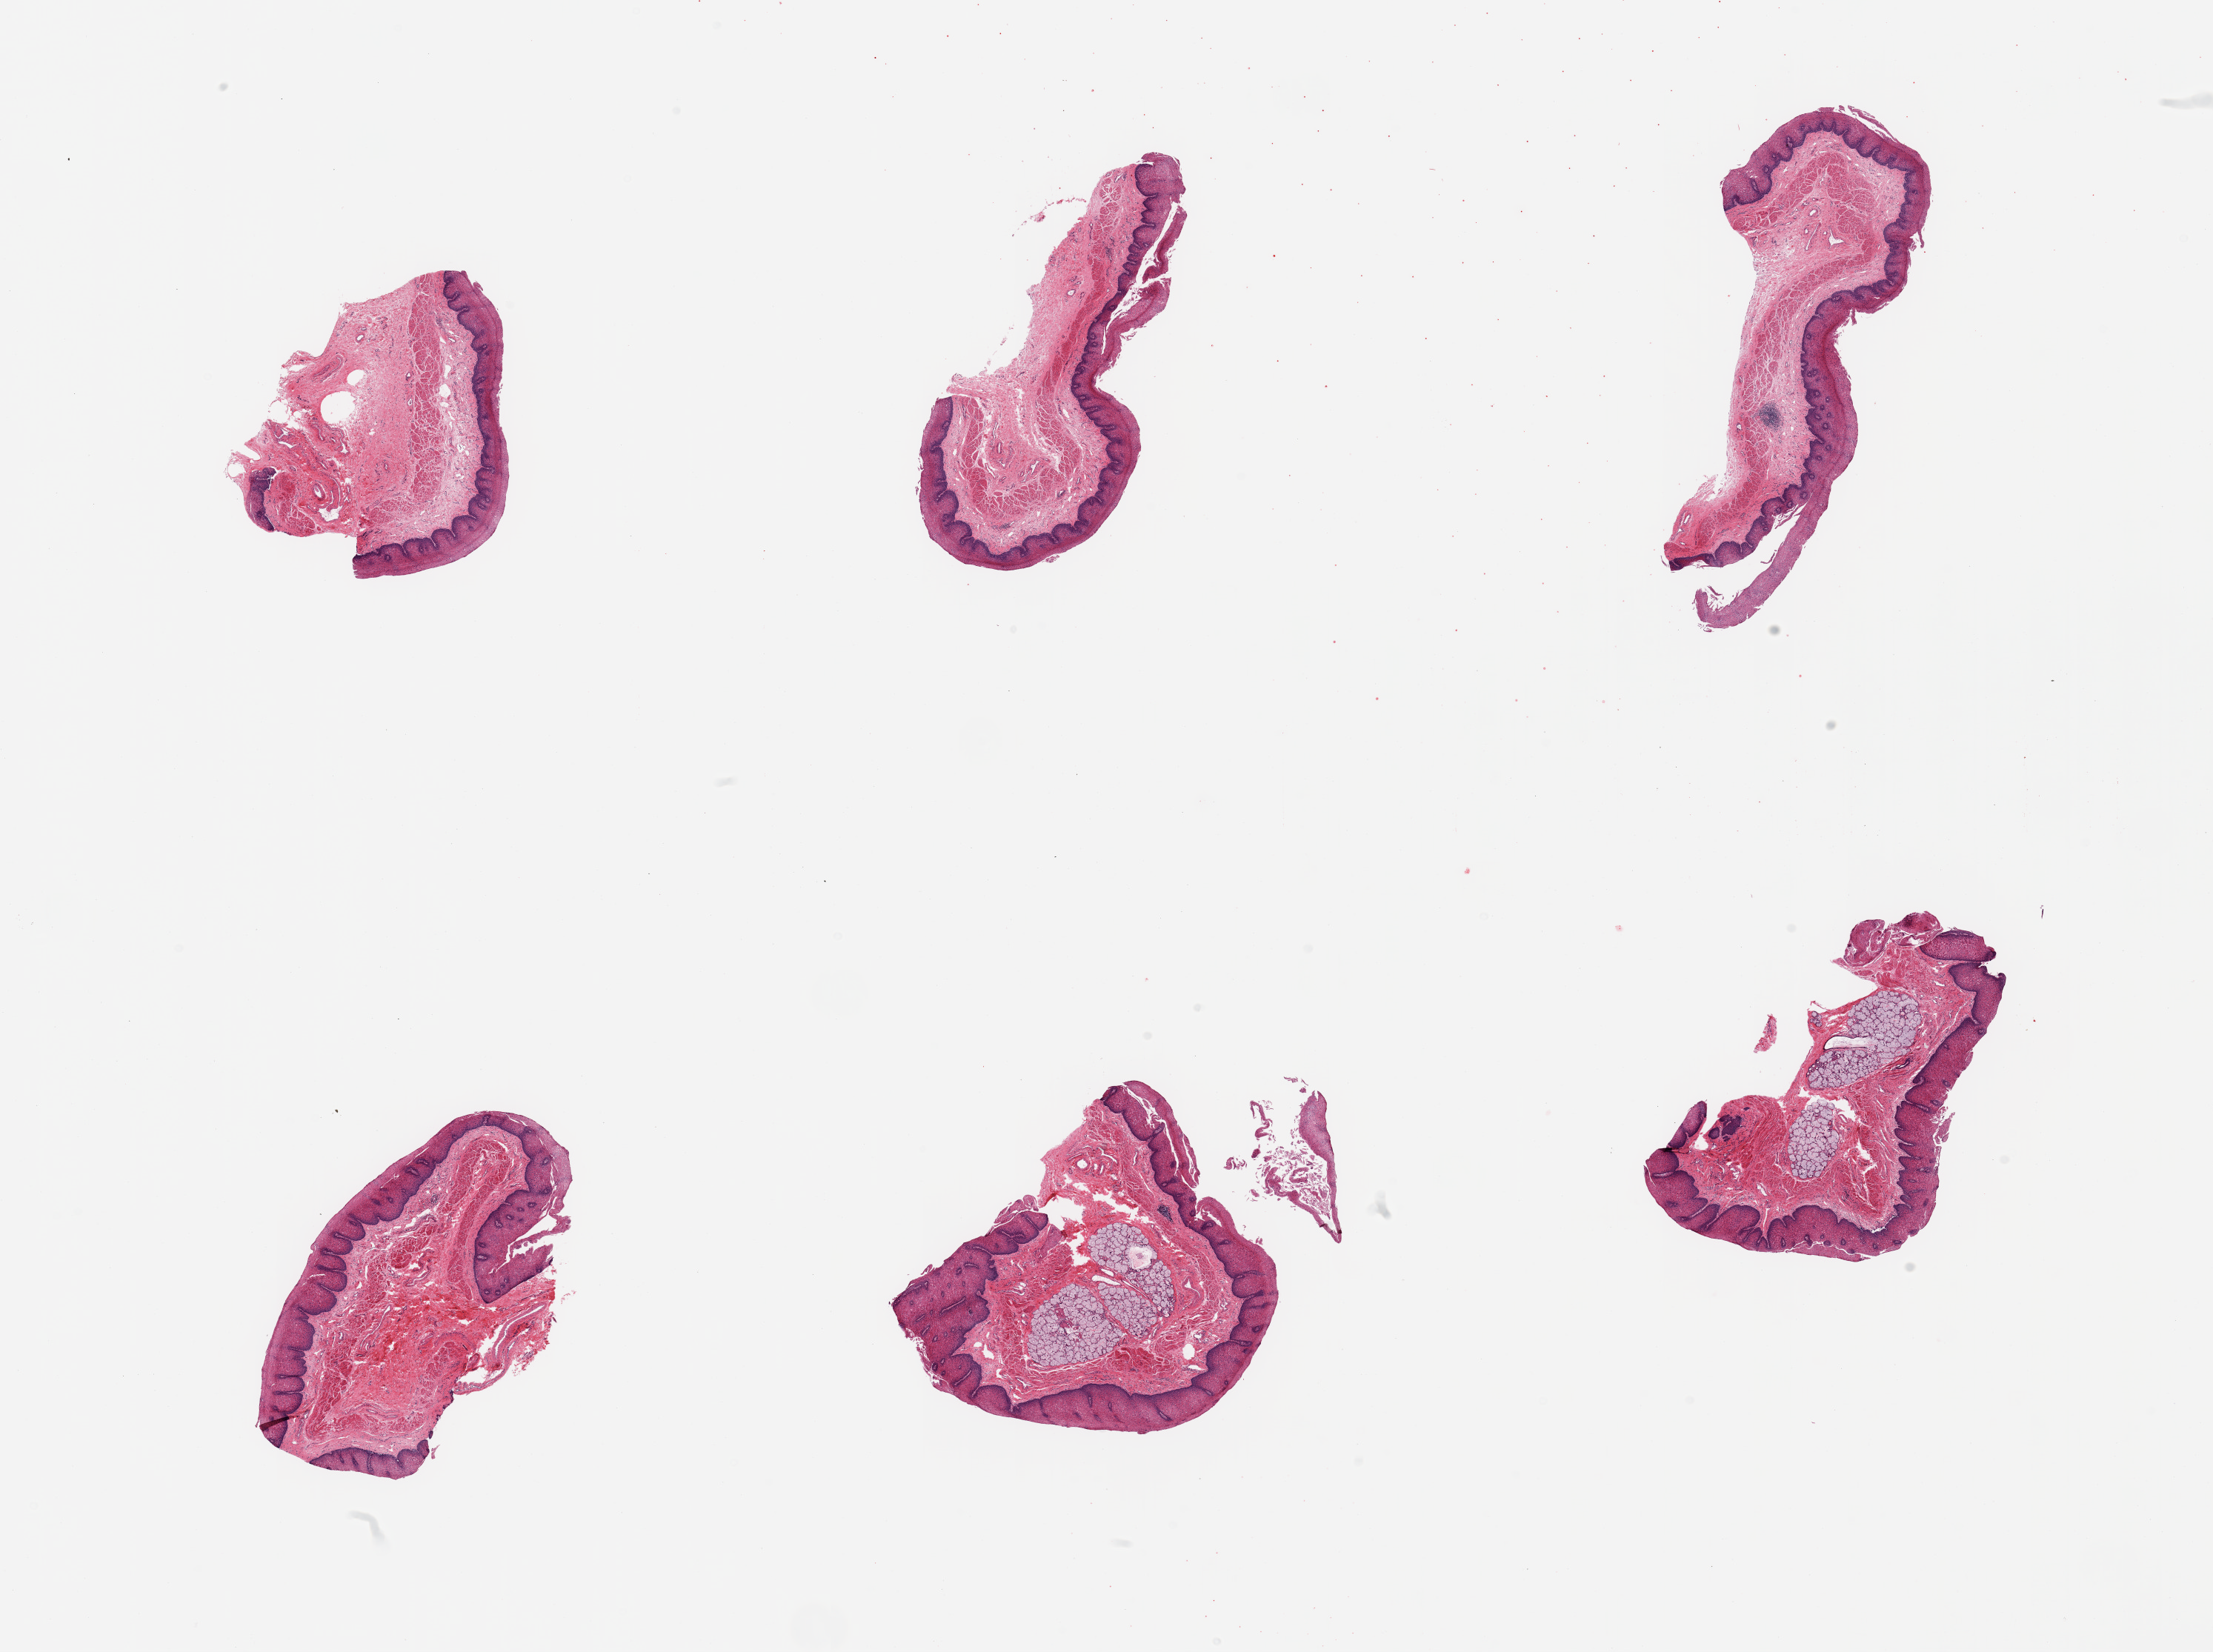
H&E whole-slide image, whole scanned area (about 23.6 x 17.6 mm, from a 20x scan) shown as a low-resolution overview, PAXgene-fixed, paraffin-embedded tissue, section of esophageal mucous membrane (target tissue), donor tissue sample. Donor: male.
Pathologist's review note for this sample: 6 pieces; 2 pieces include submucosal glands (~25%).